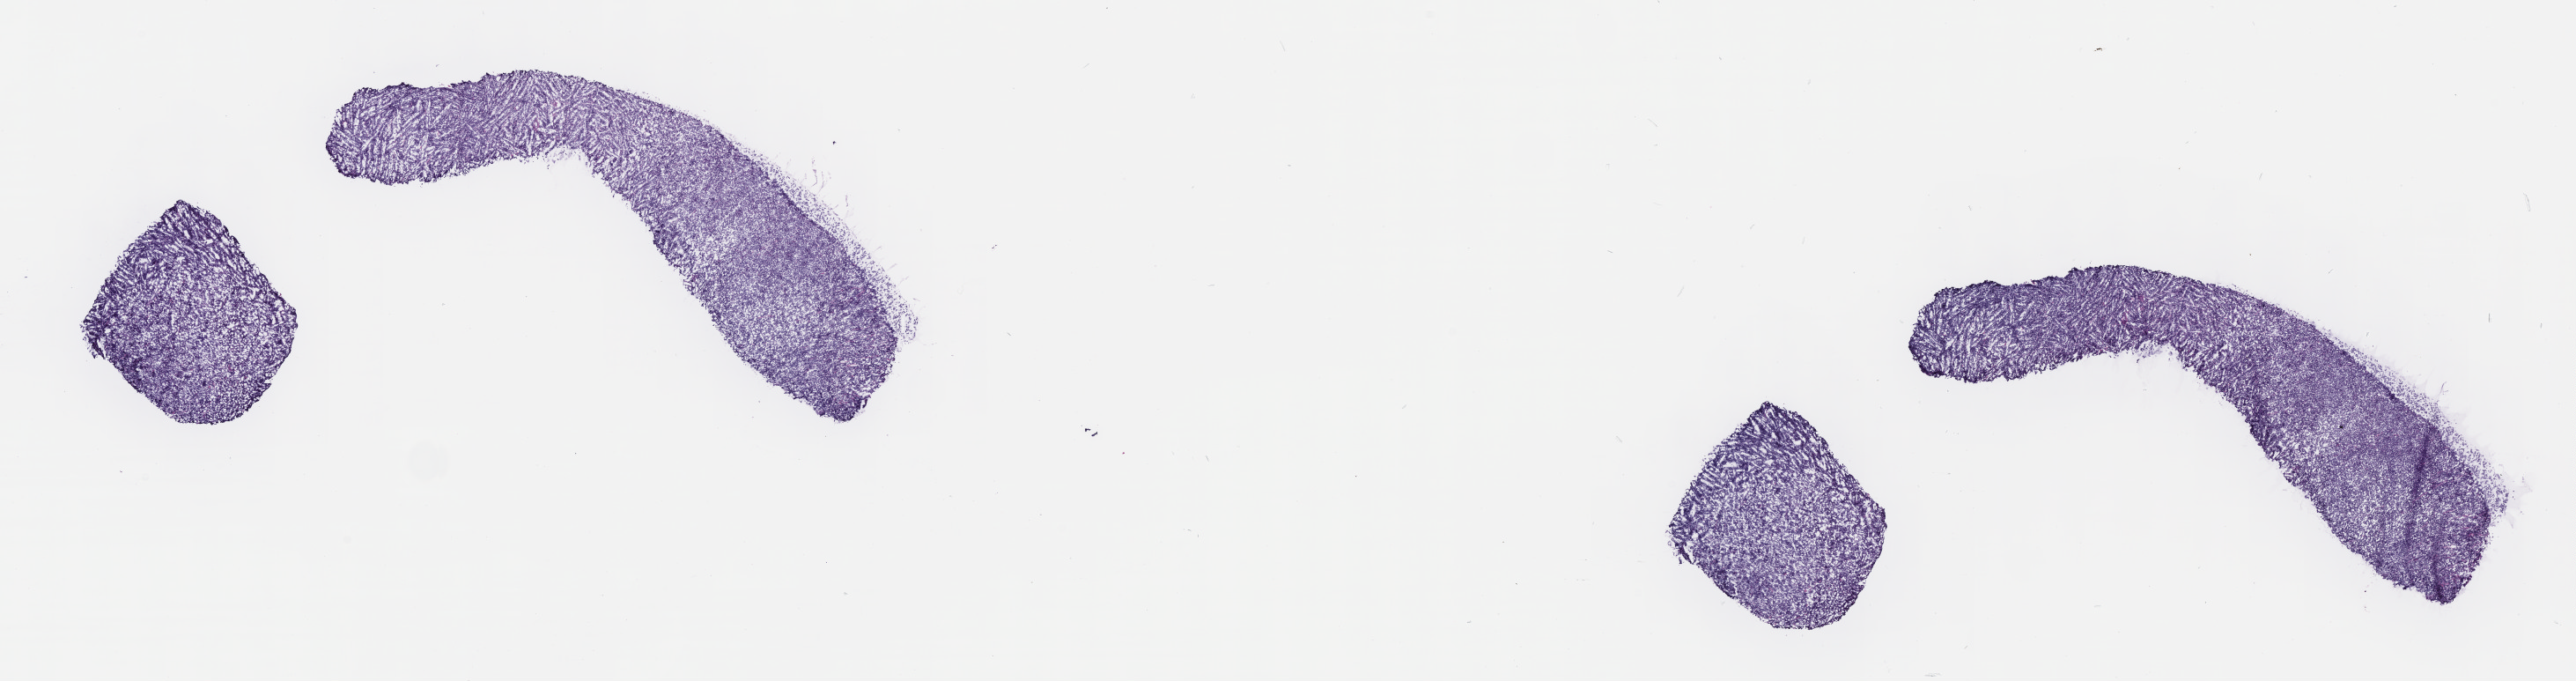
Whole-slide image, H&E stain, a low-resolution overview of the entire scanned area, about 23.6 x 6.2 mm, cryosection, primary tumor, site: cranium. Male patient; age at initial diagnosis 6 years. Slide review estimates, as recorded: tumor cells 90%, tumor nuclei 95%, stromal cells 5%, necrosis 5%, normal cells 0%. Inflammatory infiltration, as recorded: lymphocyte infiltration 70%, monocyte infiltration 15%, neutrophil infiltration 0%.
Ann Arbor stage (patient): Stage III. Section: bottom of the tissue portion. Histologic diagnosis: Burkitt lymphoma, NOS.